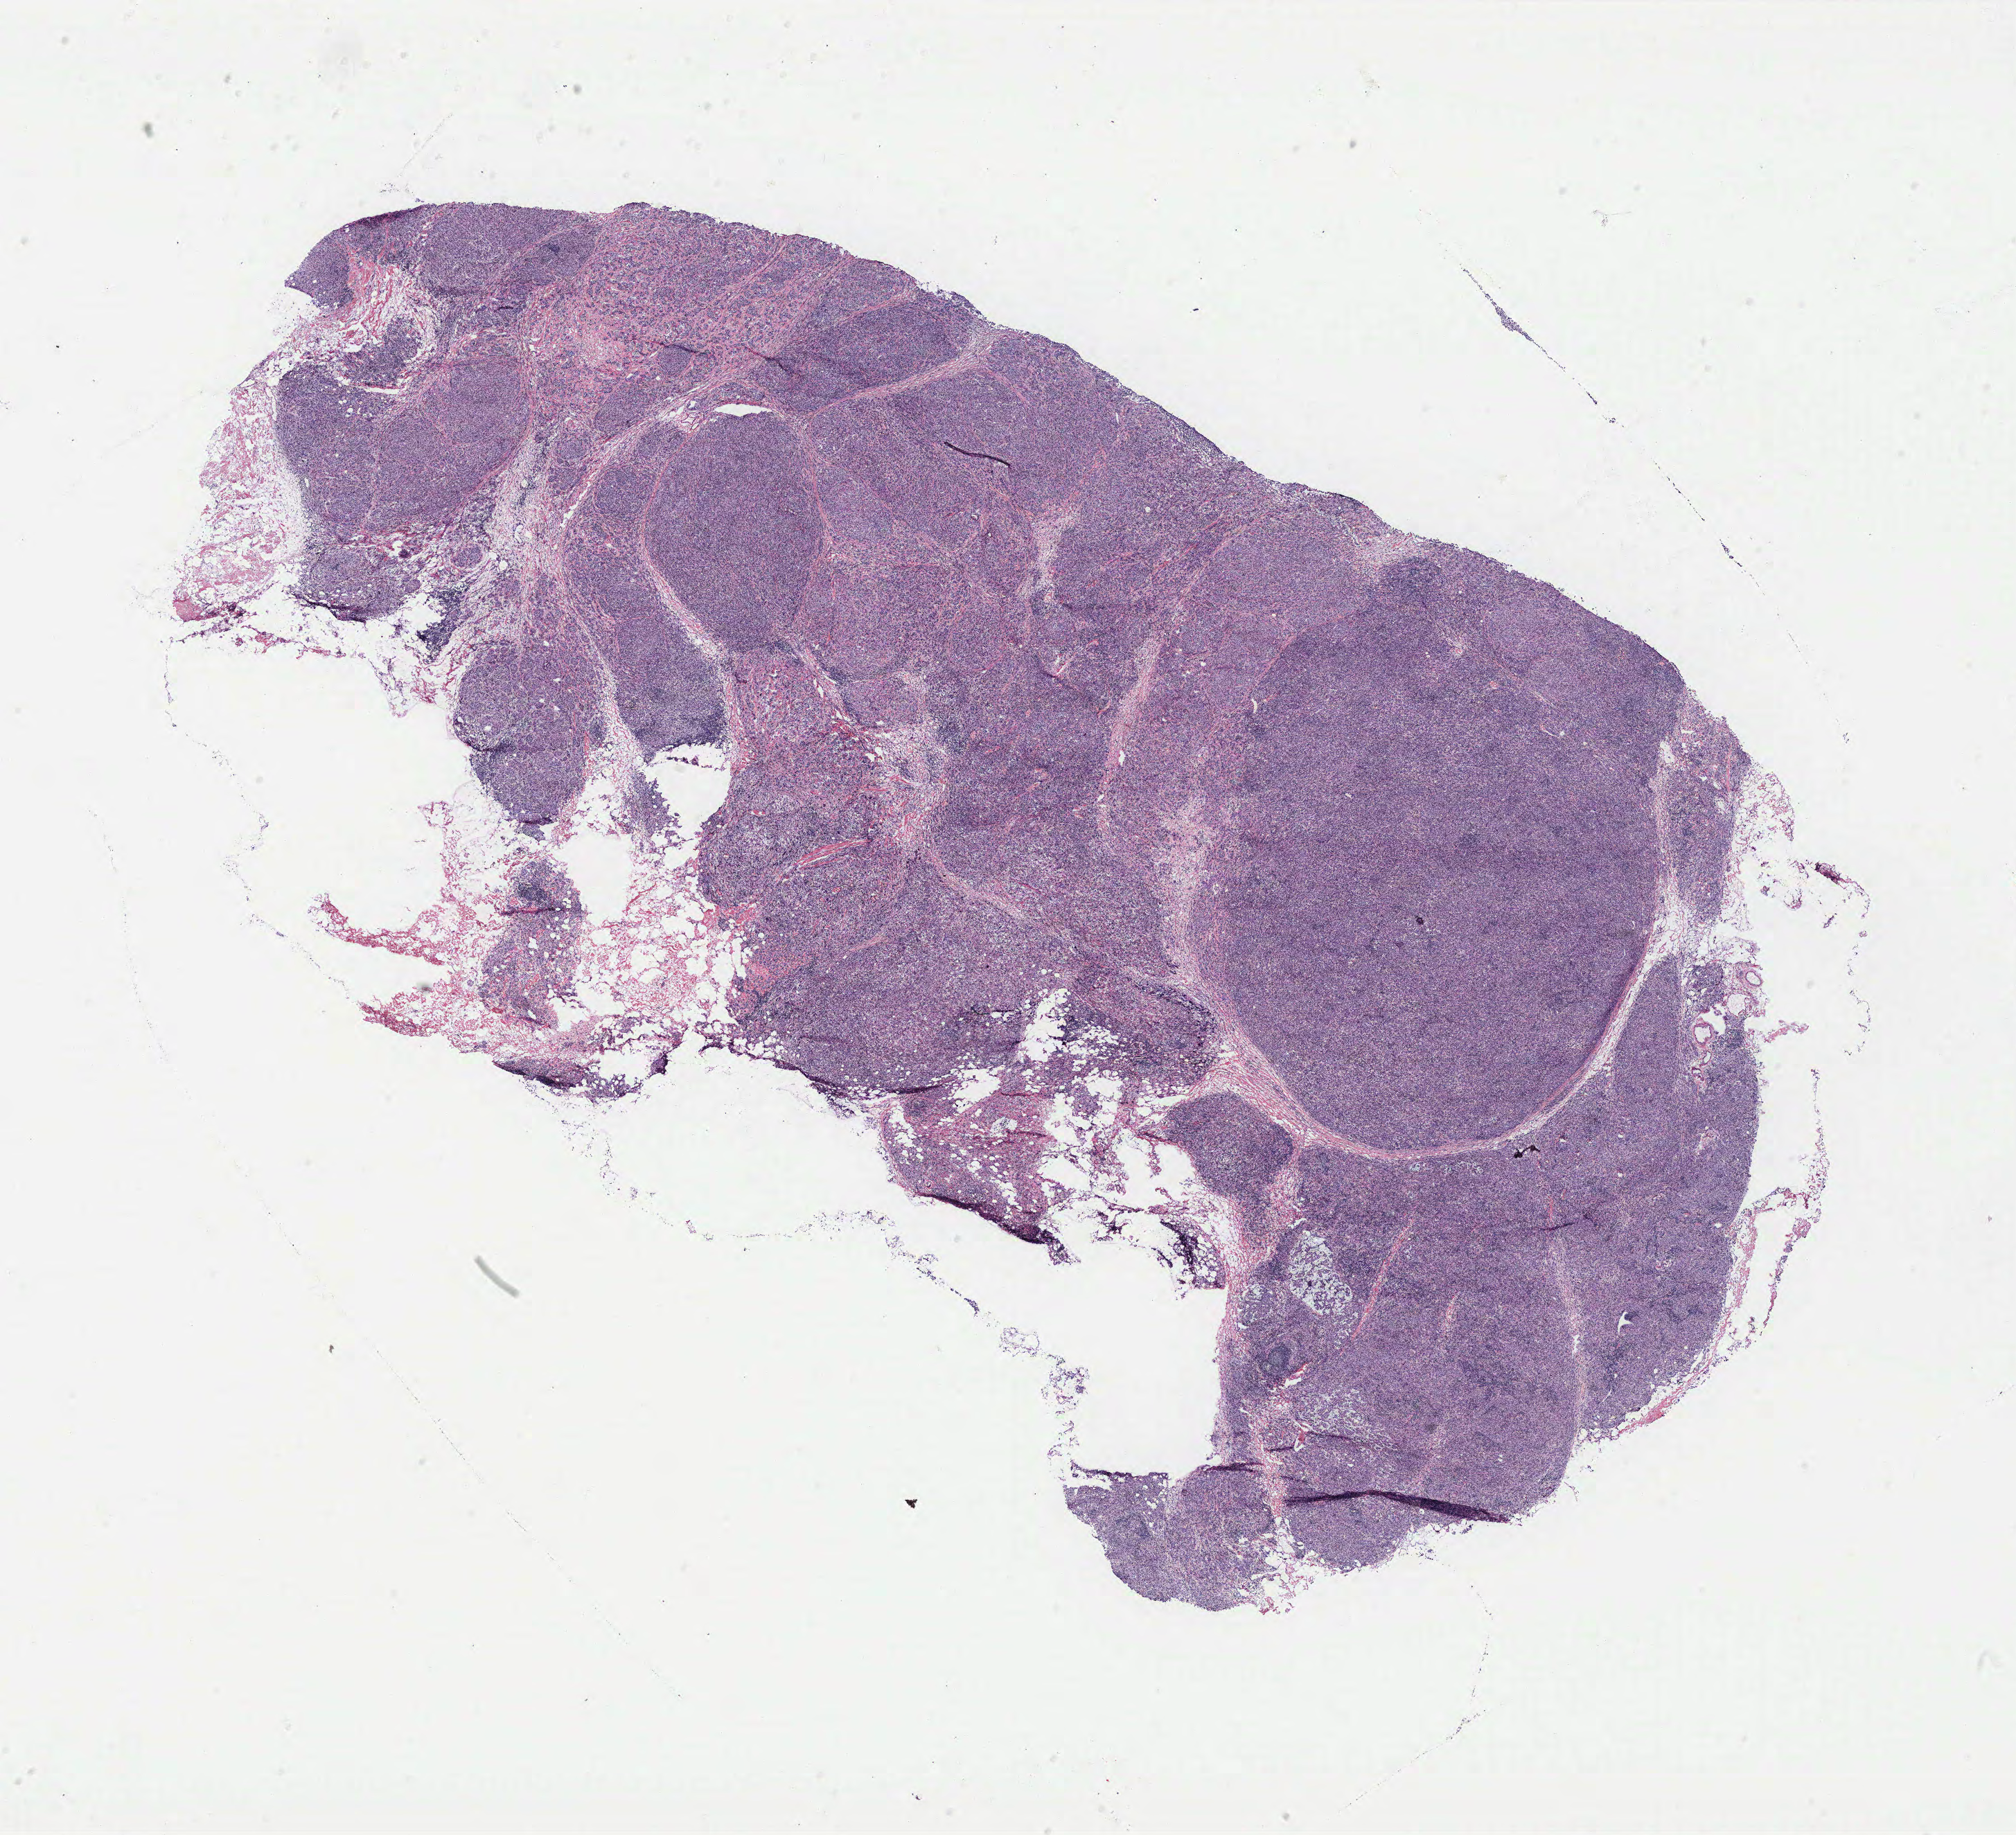
Whole-slide histology image, H&E, shown as a low-resolution overview of the whole scanned area (about 23.3 x 21.2 mm), tumour tissue sample, breast. Patient: female, age 61 years.
* diagnosis: Infiltrating duct and lobular carcinoma
* AJCC pathologic stage: IIA